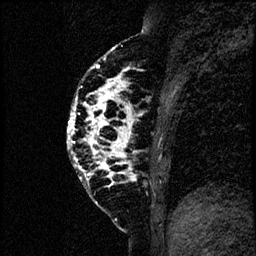
Breast MRI (dynamic contrast-enhanced), one sagittal slice. Slice 29 of 60 in the series (ordered by position). Dynamic contrast-enhanced study with each time point stored as its own series, time point 2 of 4 at this slice position (early post-contrast, ordered by acquisition time). 1.5 T. TE 4.2 ms, TR 17.6 ms. 256 × 256 image matrix, field of view 200 × 200 mm. Patient: female, 40 years. Case-level facts recorded for this patient, not image findings: setting: breast cancer imaged before/during neoadjuvant chemotherapy; receptor status: HER2-positive.
Structures marked on this image (semi-automatically segmented with operator editing):
- analysis volume of interest (the breast-tissue region the enhancement analysis was run in; not a lesion): bounding box <66,55,185,206> (left, top, right, bottom; pixels)
- tumour enhancement mask (voxels above the 100 % enhancement threshold inside the analysis volume of interest): <66,58,141,188>